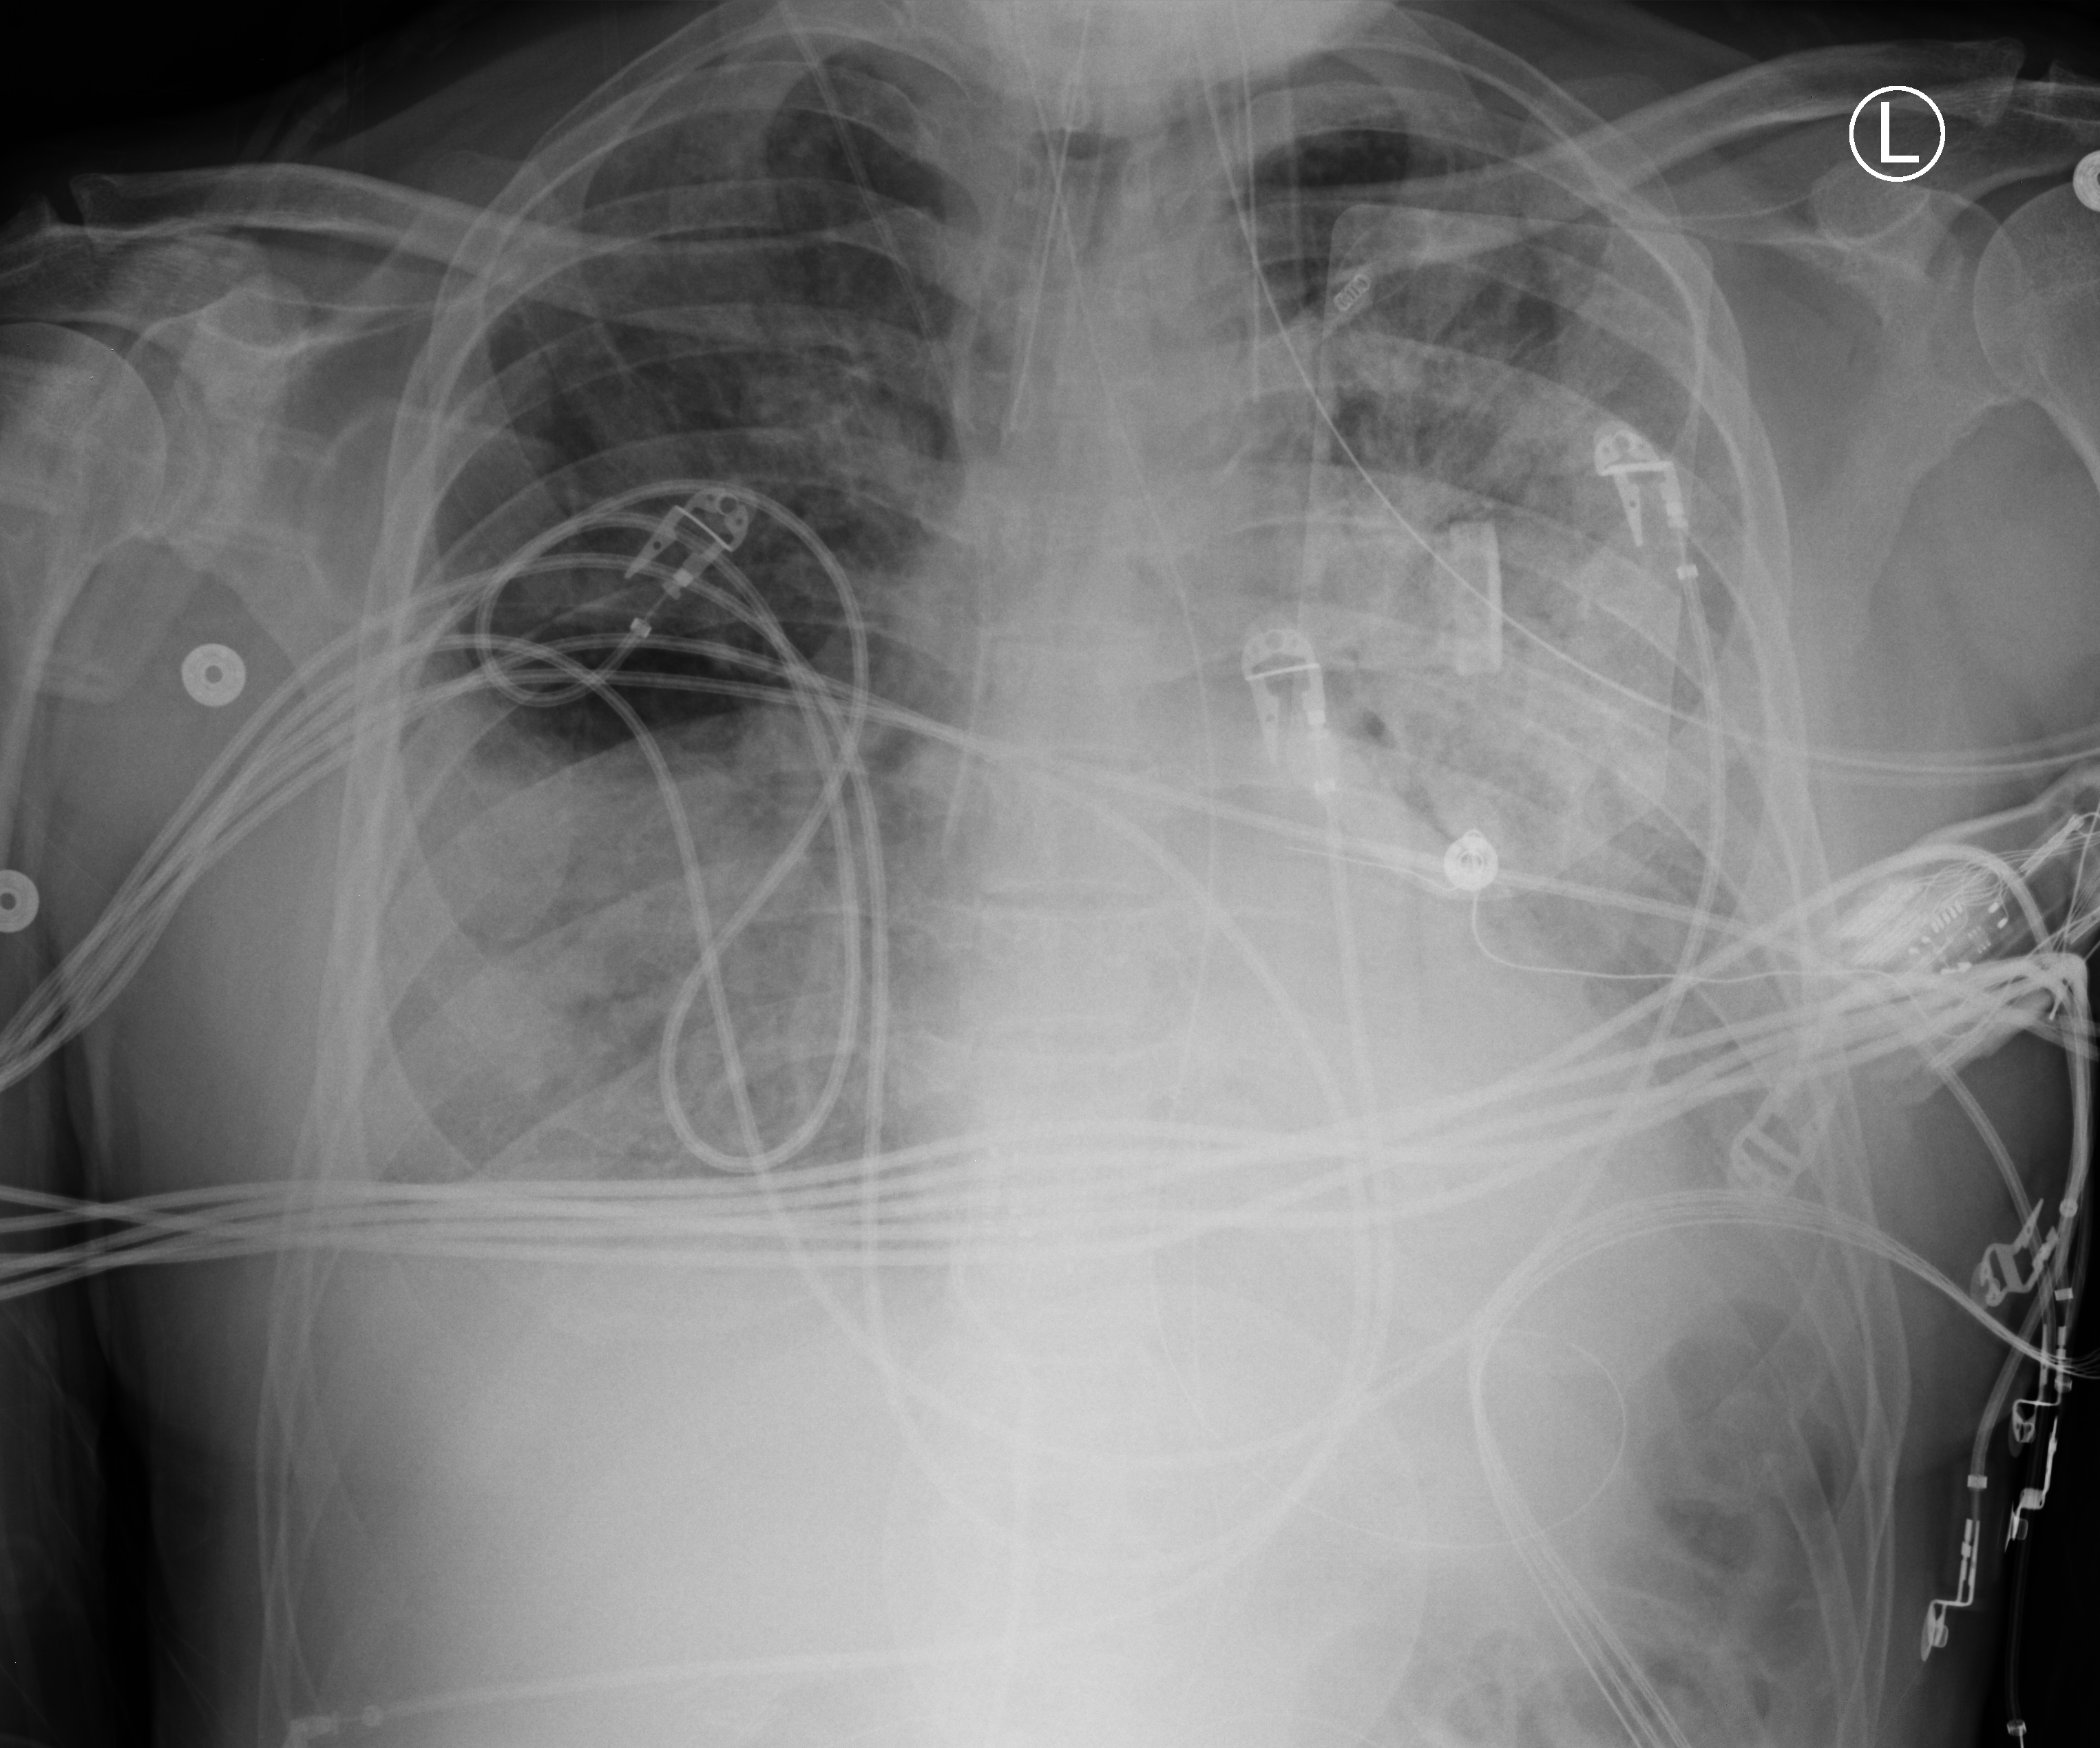
Chest X-ray (portable). Patient hospitalised with COVID-19; male, aged 60–74 years.
Admission-level facts for this patient (not findings on this image; timing relative to this image not recorded):
- hypertension (admission record): no
- mechanically ventilated during this hospital stay: yes